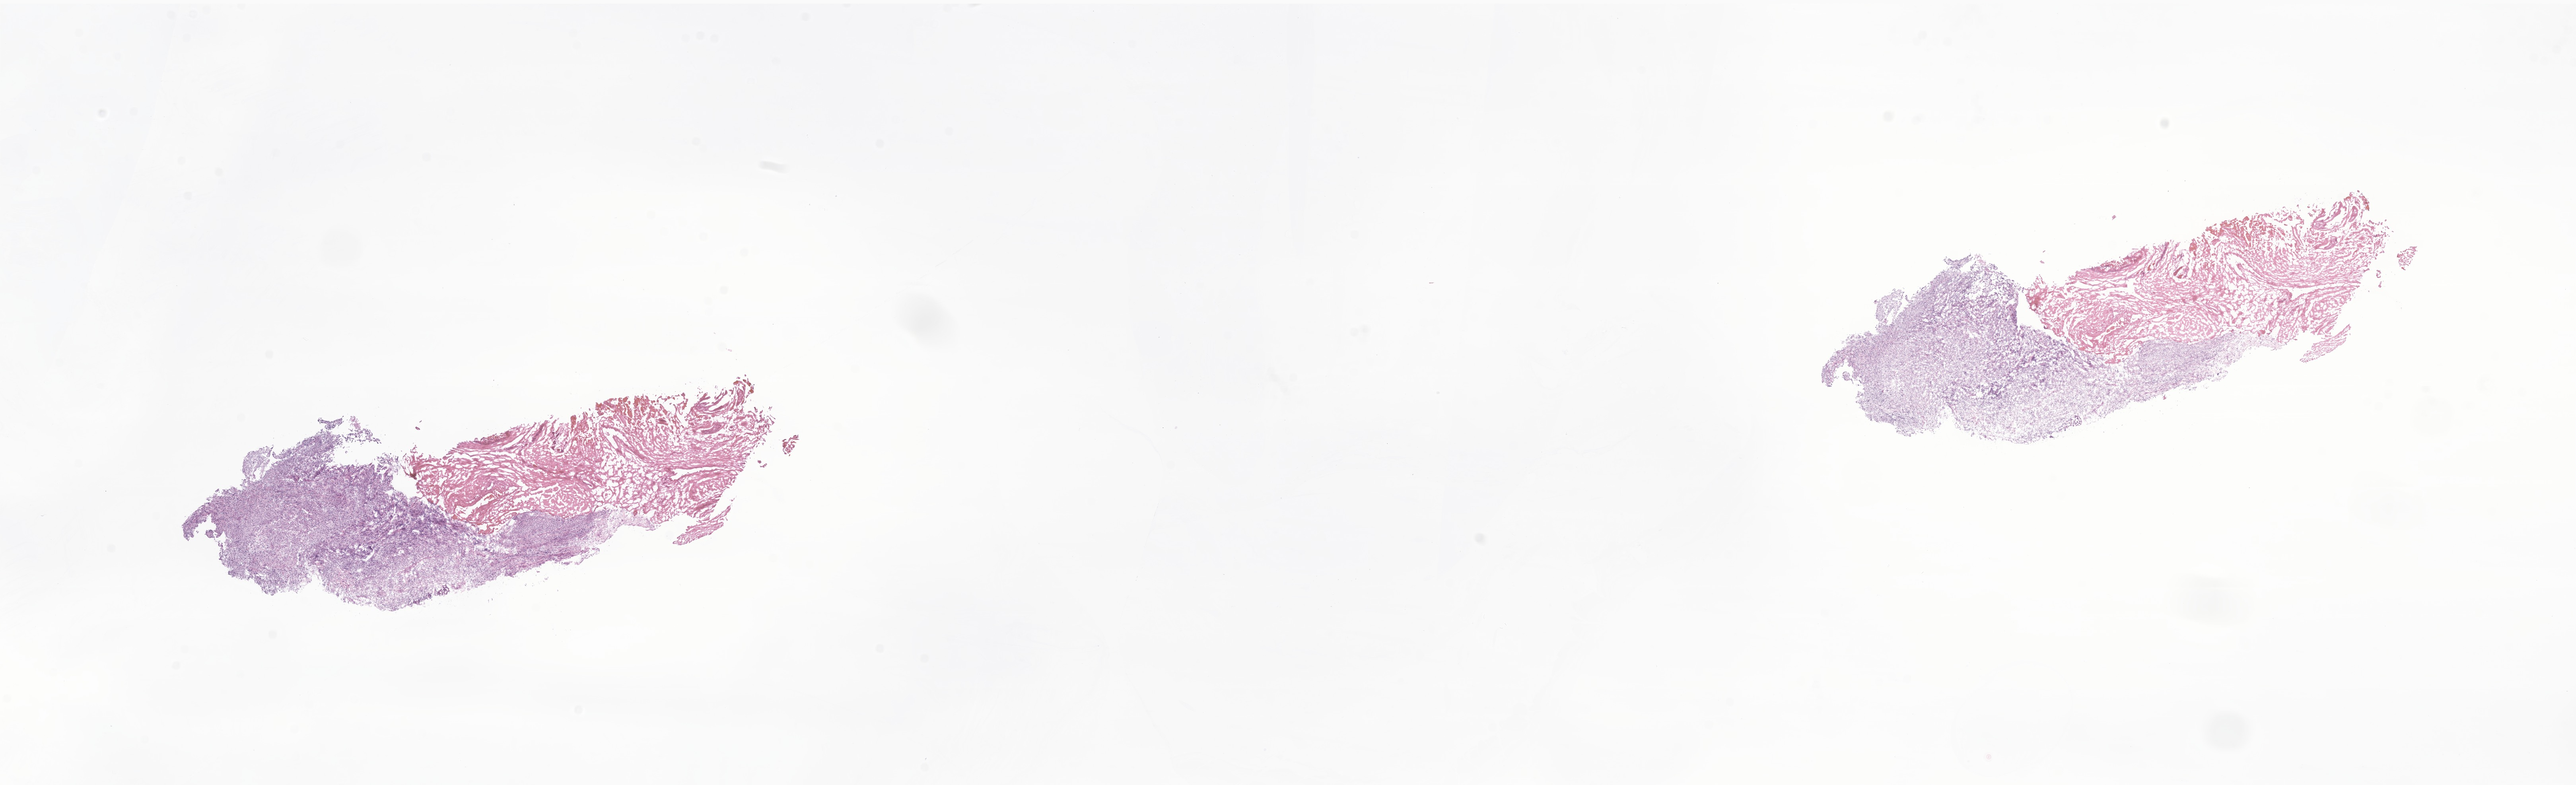
Whole-slide image, H&E stain of tumor tissue from the major salivary gland, whole scanned area (about 27.3 x 8.3 mm) shown as a low-resolution overview. Frozen section. Patient: male, age 39 months (3 years 3 months).
* recorded diagnosis: Spindle cell rhabdomyosarcoma